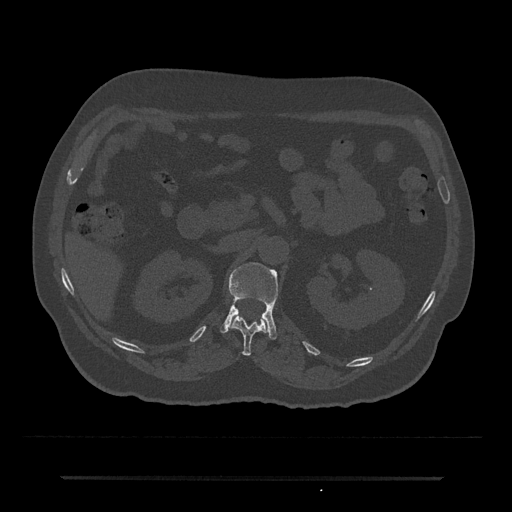
CT including the spine, one axial slice. Position 97 of 797 along the scan axis. 120 kVp. Bone window (W 1800 / L 400 HU). 0.5 mm slice thickness. 512 × 512 image matrix, field of view 437 × 437 mm. Patient: male, 69 years. Case-level facts recorded for this patient, not image findings: primary cancer: prostate.
Structures marked on this image (semi-automatic segmentation, software-assisted and operator-edited):
- L1 vertebra: bounding box <220,262,278,340> (left, top, right, bottom; pixels)
- T12 vertebra: <231,313,268,355>